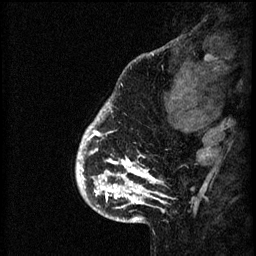
Breast MRI (dynamic contrast-enhanced), one sagittal slice; position 12 of 60 along the scan axis; 3 images stored at this slice position (order not interpretable as contrast timing); 1.5 T; TE 4.2 ms, TR 8.2 ms; 2 mm slice thickness; 256 × 256 image matrix, field of view 180 × 180 mm. Patient: female, 41 years.
Structures marked on this image (semi-automatic segmentation, software-assisted and operator-edited):
- analysis volume of interest (the breast-tissue region the enhancement analysis was run in; not a lesion): bounding box (x1, y1, x2, y2) in pixels: (77, 110, 176, 205)
- tumour enhancement mask (voxels above the 70 % enhancement threshold inside the analysis volume of interest): (77, 112, 165, 205)